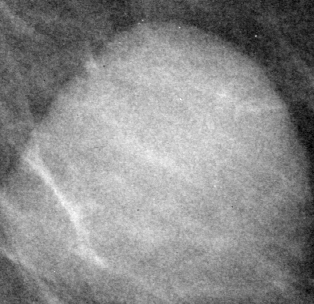
Crop from a digitized film mammogram around one marked abnormality, left breast, MLO view.
Marked abnormality: mass, shape oval, margins circumscribed; BI-RADS assessment category 4; pathology result (as recorded, not read from the image): benign.